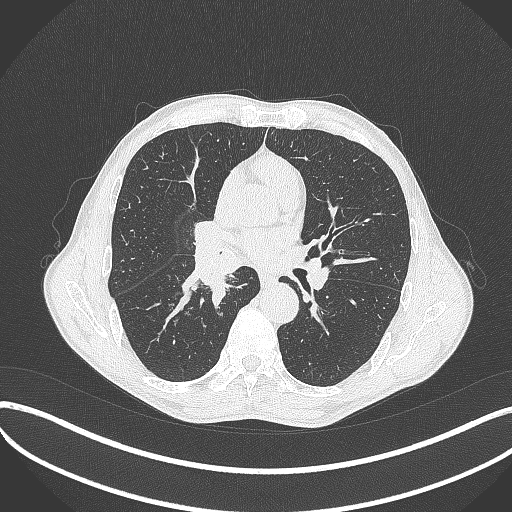
Chest CT, one axial slice; slice 231 of 481 in the series (ordered by position); 120 kVp; lung window (W 1500 / L -600 HU); 1 mm slice thickness; 512 × 512 image matrix. Patient: male, 65 years. From the clinical record (not read from this slice): clinical TNM (as recorded): T2a N0 M0; histopathological grade: G2.
Structures marked on this image (bounding box drawn by a radiologist):
- lung tumour (recorded histology: squamous cell carcinoma): bounding box <181,221,242,293> (left, top, right, bottom; pixels)